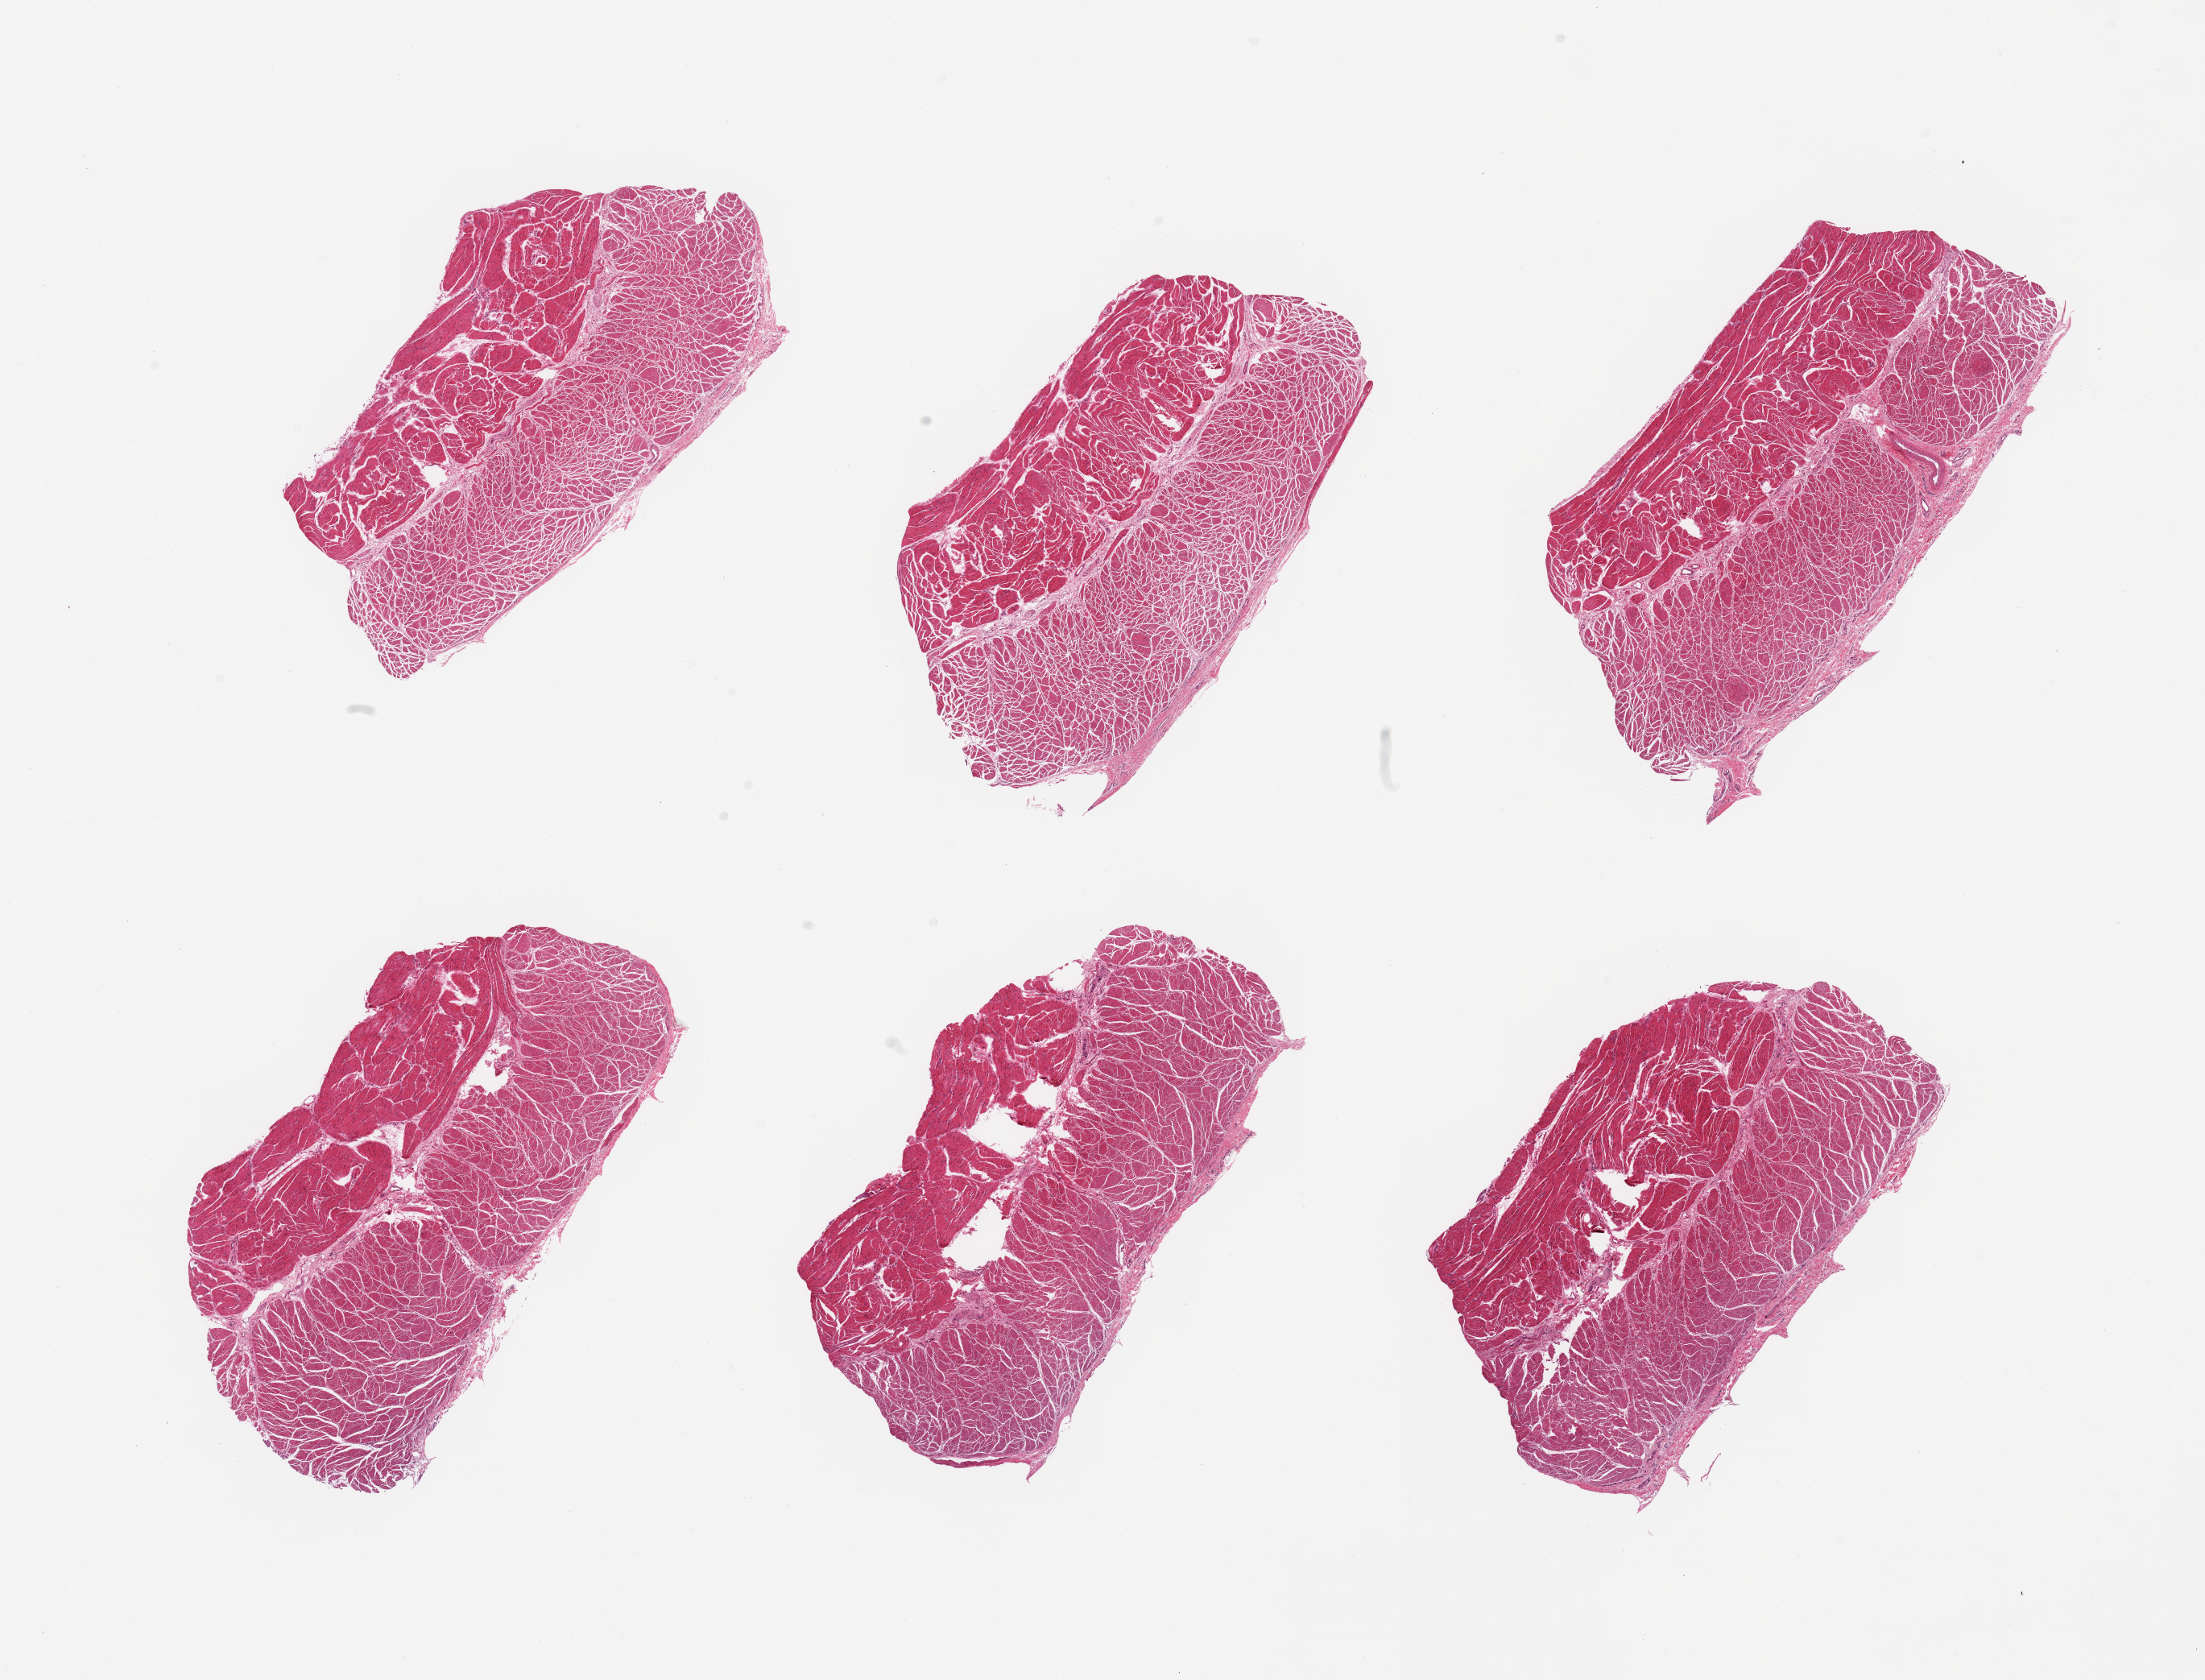
H&E whole-slide image, brightfield, low-resolution overview of the scanned area, about 21.7 x 16.5 mm, PAXgene-fixed paraffin-embedded (PFPE) section, sampled site (target tissue): esophageal muscle, donor tissue sample. Donor sex: male.
* reviewer comment on this tissue sample: 6 pieces, confirmed target muscularis